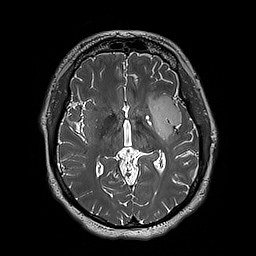
Brain MRI from a brain-tumour surgery series, one axial slice. Position 107 of 192 along the scan axis. 1 mm slice thickness. 256 × 256 image matrix. From the clinical record (not read from this slice): histopathology: Astrocytoma; WHO grade: 3; IDH mutation: yes; tumour location: Left Insular.
Outlined on this slice (expert manual segmentation):
- tumour: bounding box (x1, y1, x2, y2) in pixels: (148, 95, 181, 141)